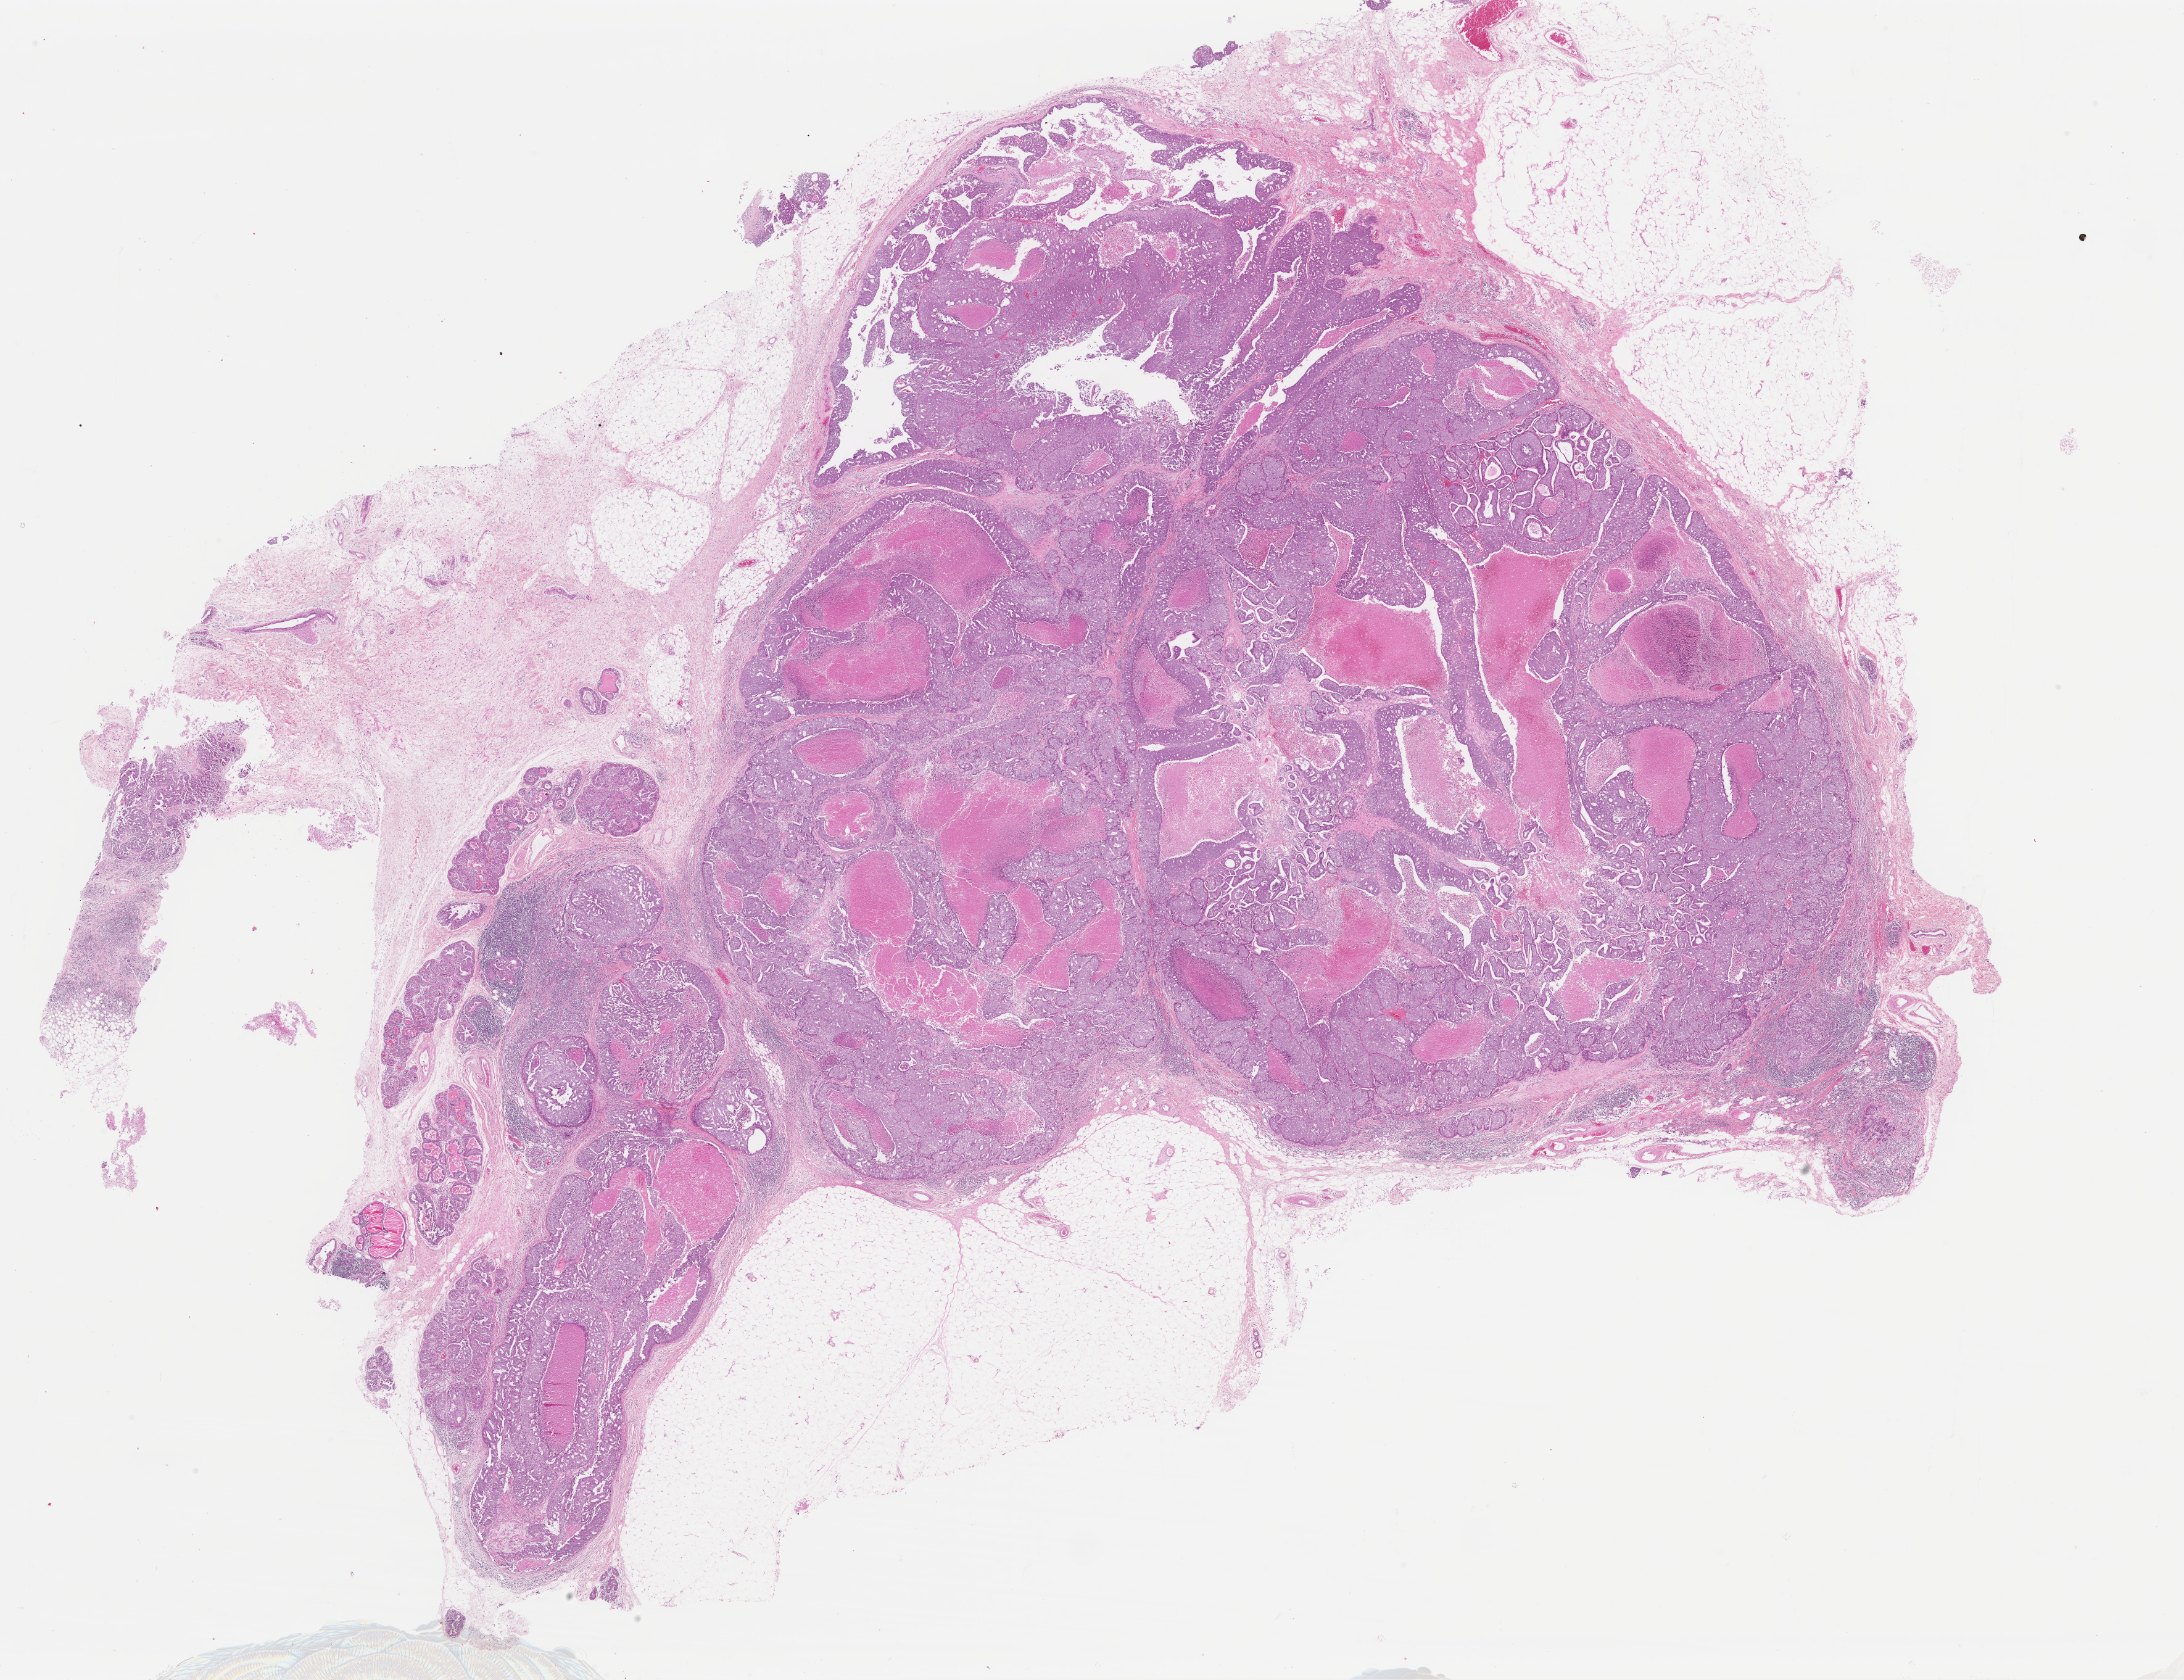
Digitized H&E-stained tissue section (whole slide), shown as a low-resolution overview of the whole scanned area (about 28.0 x 21.5 mm, from a 40x scan). Formalin-fixed paraffin-embedded (FFPE) diagnostic section. Breast, primary tumour sample. Female, age 73 years at initial diagnosis.
* lymph nodes positive (case pathology): 0 of 7 examined
* laterality: left
* AJCC pathologic stage: IIA
* pathologic diagnosis: Infiltrating duct carcinoma, NOS